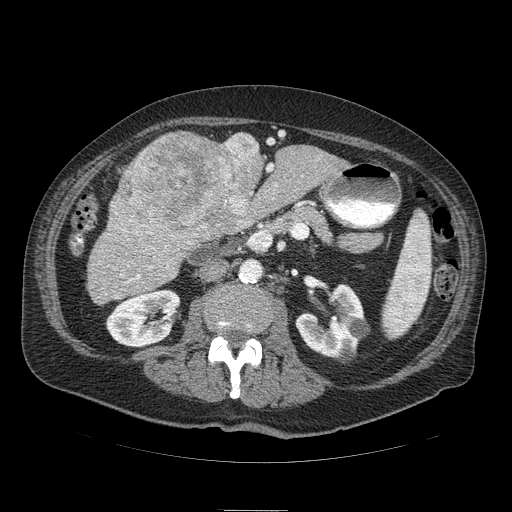
Contrast-enhanced abdominal CT (liver protocol), one axial slice. Slice 33 of 103 in the series (ordered by position). Soft-tissue window (W 400 / L 40 HU). 2.5 mm slice thickness. 512 × 512 image matrix, field of view 440 × 440 mm. From the clinical record (not read from this slice): diagnosis: hepatocellular carcinoma (patient treated with transarterial chemoembolisation; whether this scan precedes or follows treatment is not stated here); TNM stage (as recorded): Stage-IIIA; Child-Pugh class: B.
Annotated regions visible in this slice (semi-automatic segmentation, software-assisted and operator-edited):
- liver parenchyma outside the tumour (the mass and vessels are separate outlines, so this box may not span the whole liver): box from (x=96, y=134) to (x=344, y=284) px
- mass: (x=110, y=130)–(x=264, y=252)
- liver vessels: (x=150, y=164)–(x=273, y=268)